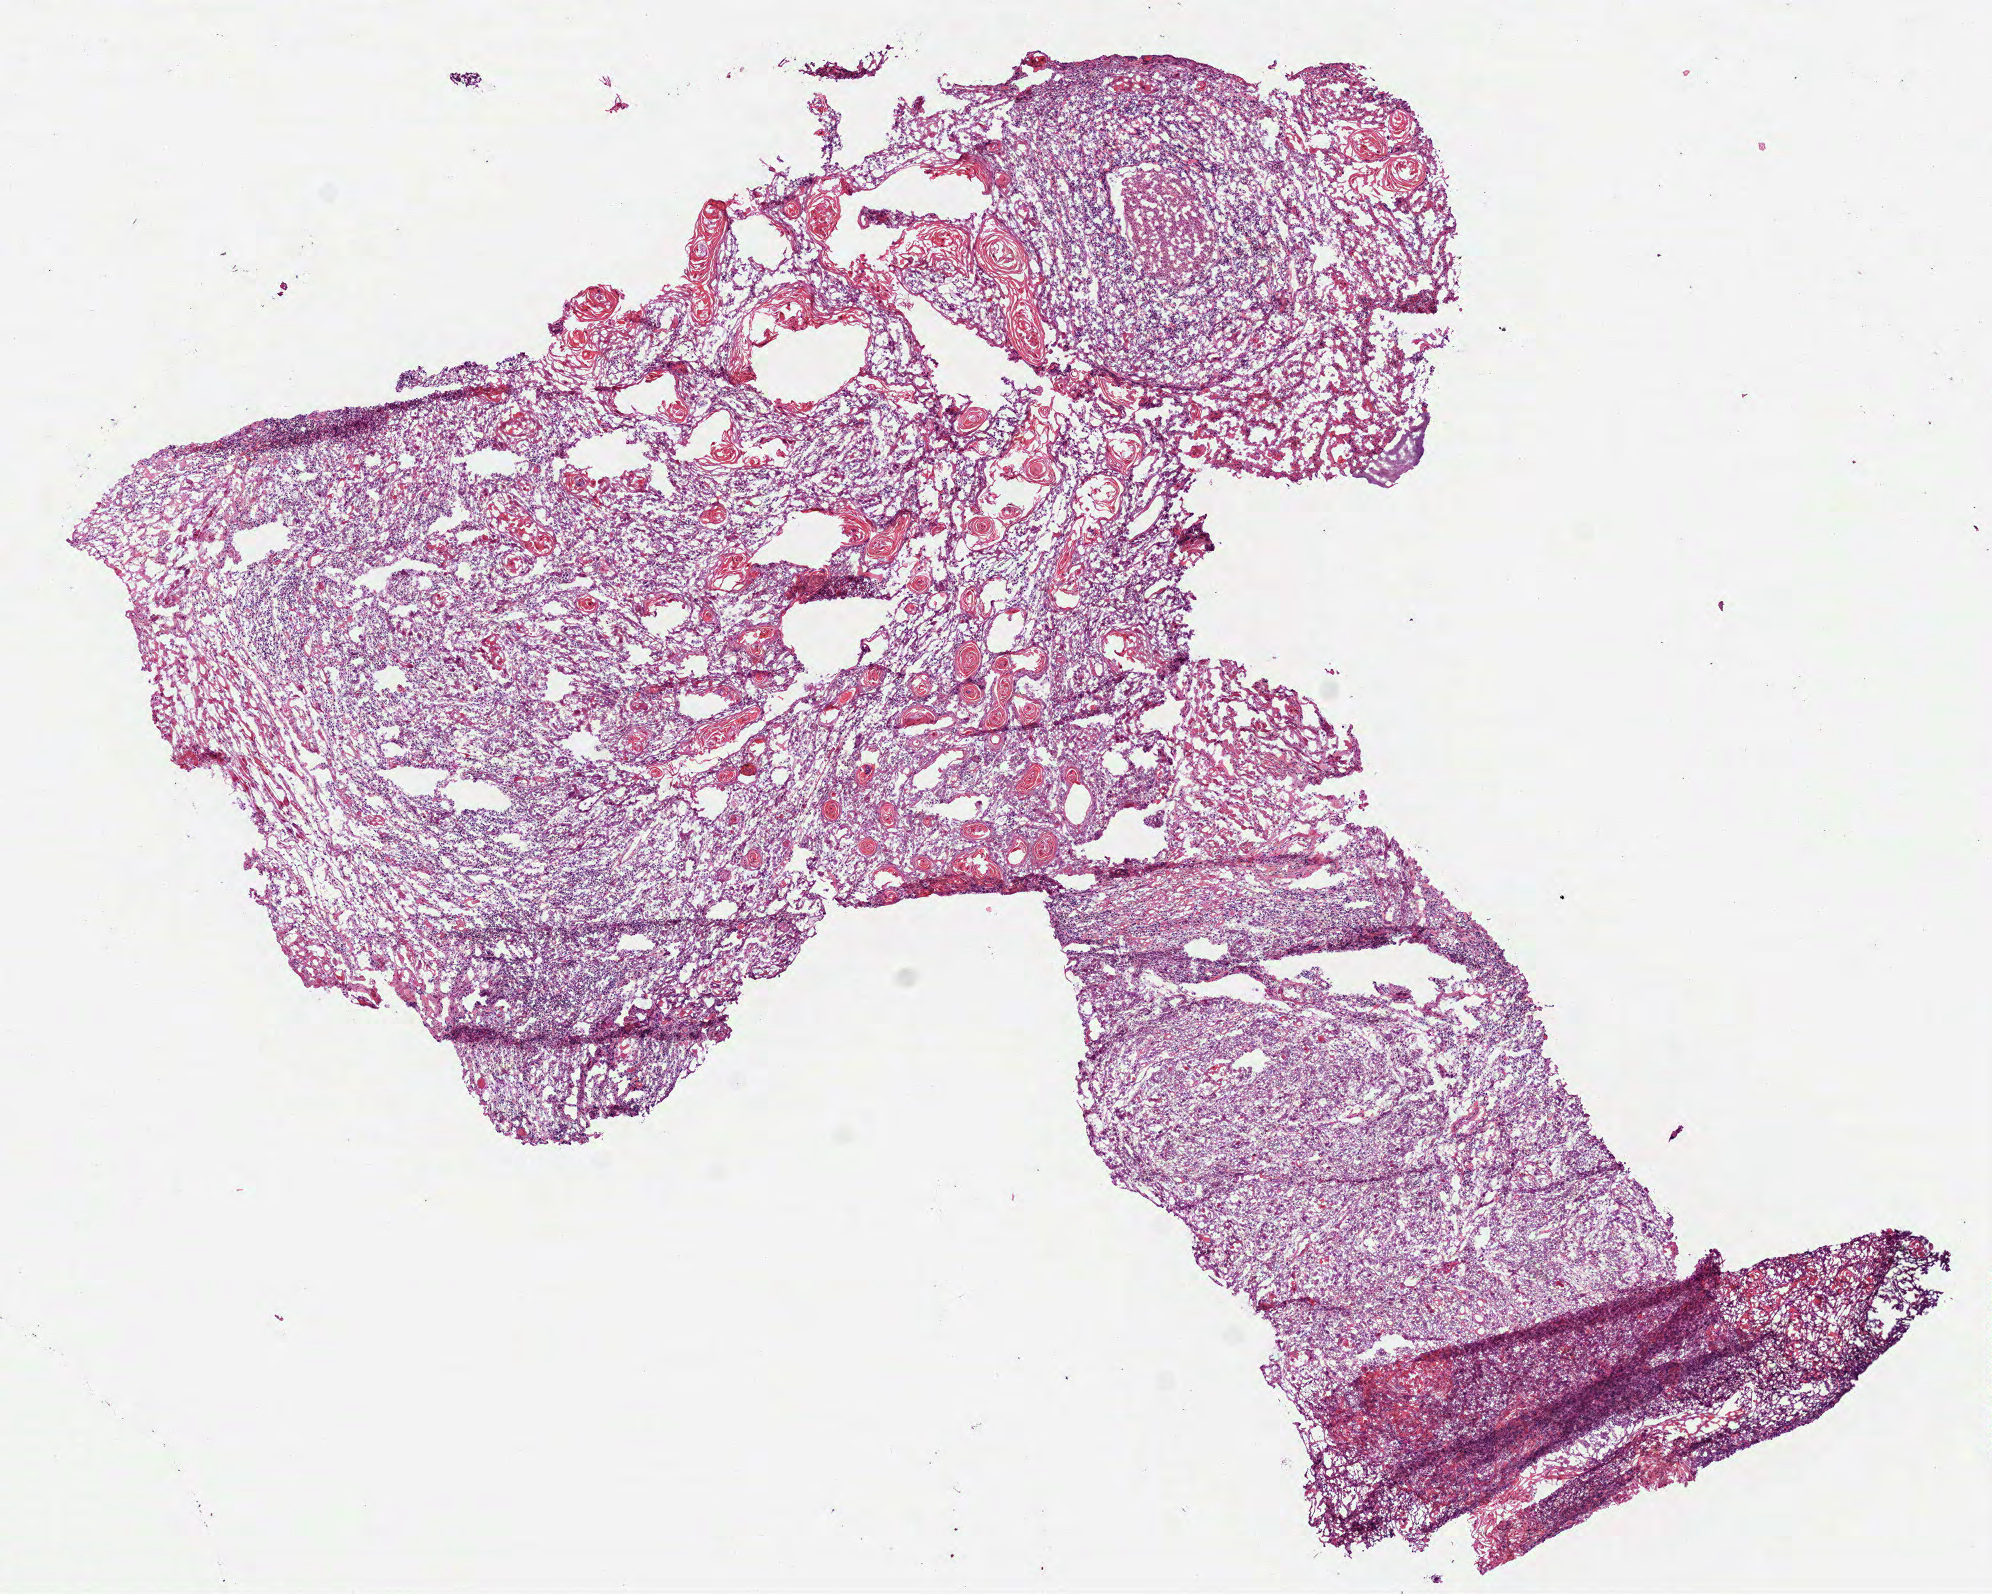
Whole-slide histology image, H&E-stained — low-resolution overview of the scanned area, about 8.0 x 6.4 mm (from a 40x scan); frozen section from the bottom of the tissue portion; sample: primary tumour, head and neck. Female, age 58 years at initial diagnosis. Pathologist review of this section (percent, as recorded): tumour cells 90%, tumour nuclei 50%.
Histologic diagnosis: Squamous cell carcinoma, NOS (tongue, NOS).